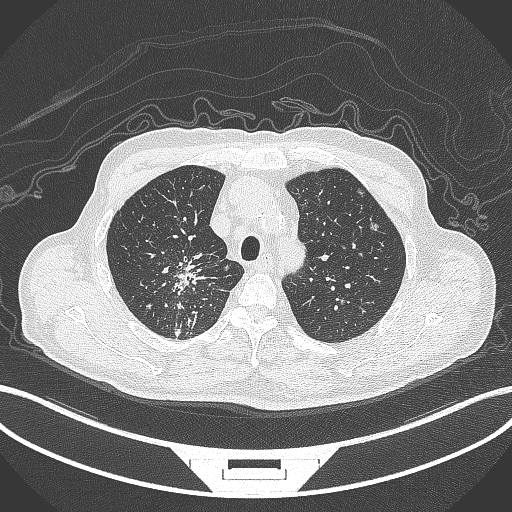
Chest CT, one axial slice. Position 297 of 407 along the scan axis. Reconstruction kernel B70f. 120 kVp. Lung window (W 1500 / L -600 HU). 1 mm slice thickness. 512 × 512 image matrix. Patient: male, 69 years. Case-level facts recorded for this patient, not image findings: clinical TNM (as recorded): T1c N1 M1.
Outlined on this slice (rectangle marked by the reading radiologist):
- lung tumour (recorded histology: adenocarcinoma): bounding box <166,252,213,307> (left, top, right, bottom; pixels)